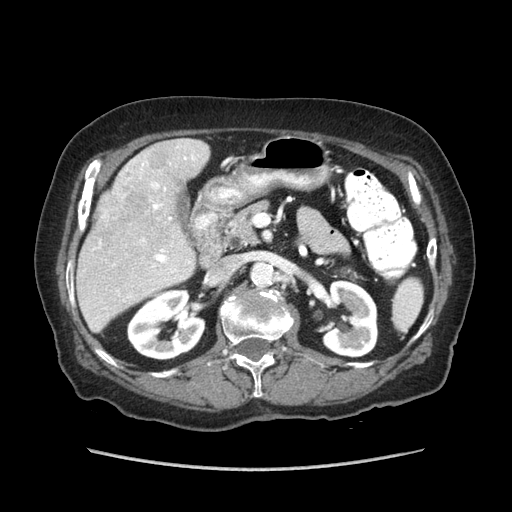
Contrast-enhanced abdominal CT (liver protocol), one axial slice. Slice 34 of 89 in the series (ordered by position). Reconstruction kernel STANDARD. 140 kVp. Soft-tissue window (W 400 / L 40 HU). 2.5 mm slice thickness. 512 × 512 image matrix, field of view 360 × 360 mm. From the clinical record (not read from this slice): diagnosis: hepatocellular carcinoma (patient treated with transarterial chemoembolisation; whether this scan precedes or follows treatment is not stated here); TNM stage (as recorded): Stage-IIIA; Child-Pugh class: A; tumour differentiation: well differentiated; tumour nodularity: multinodular.
Outlined on this slice (semi-automatically segmented with operator editing):
- liver parenchyma outside the tumour (the mass and vessels are separate outlines, so this box may not span the whole liver): bounding box <76,138,210,332> (left, top, right, bottom; pixels)
- mass: <92,154,157,242>
- liver vessels: <99,155,196,273>